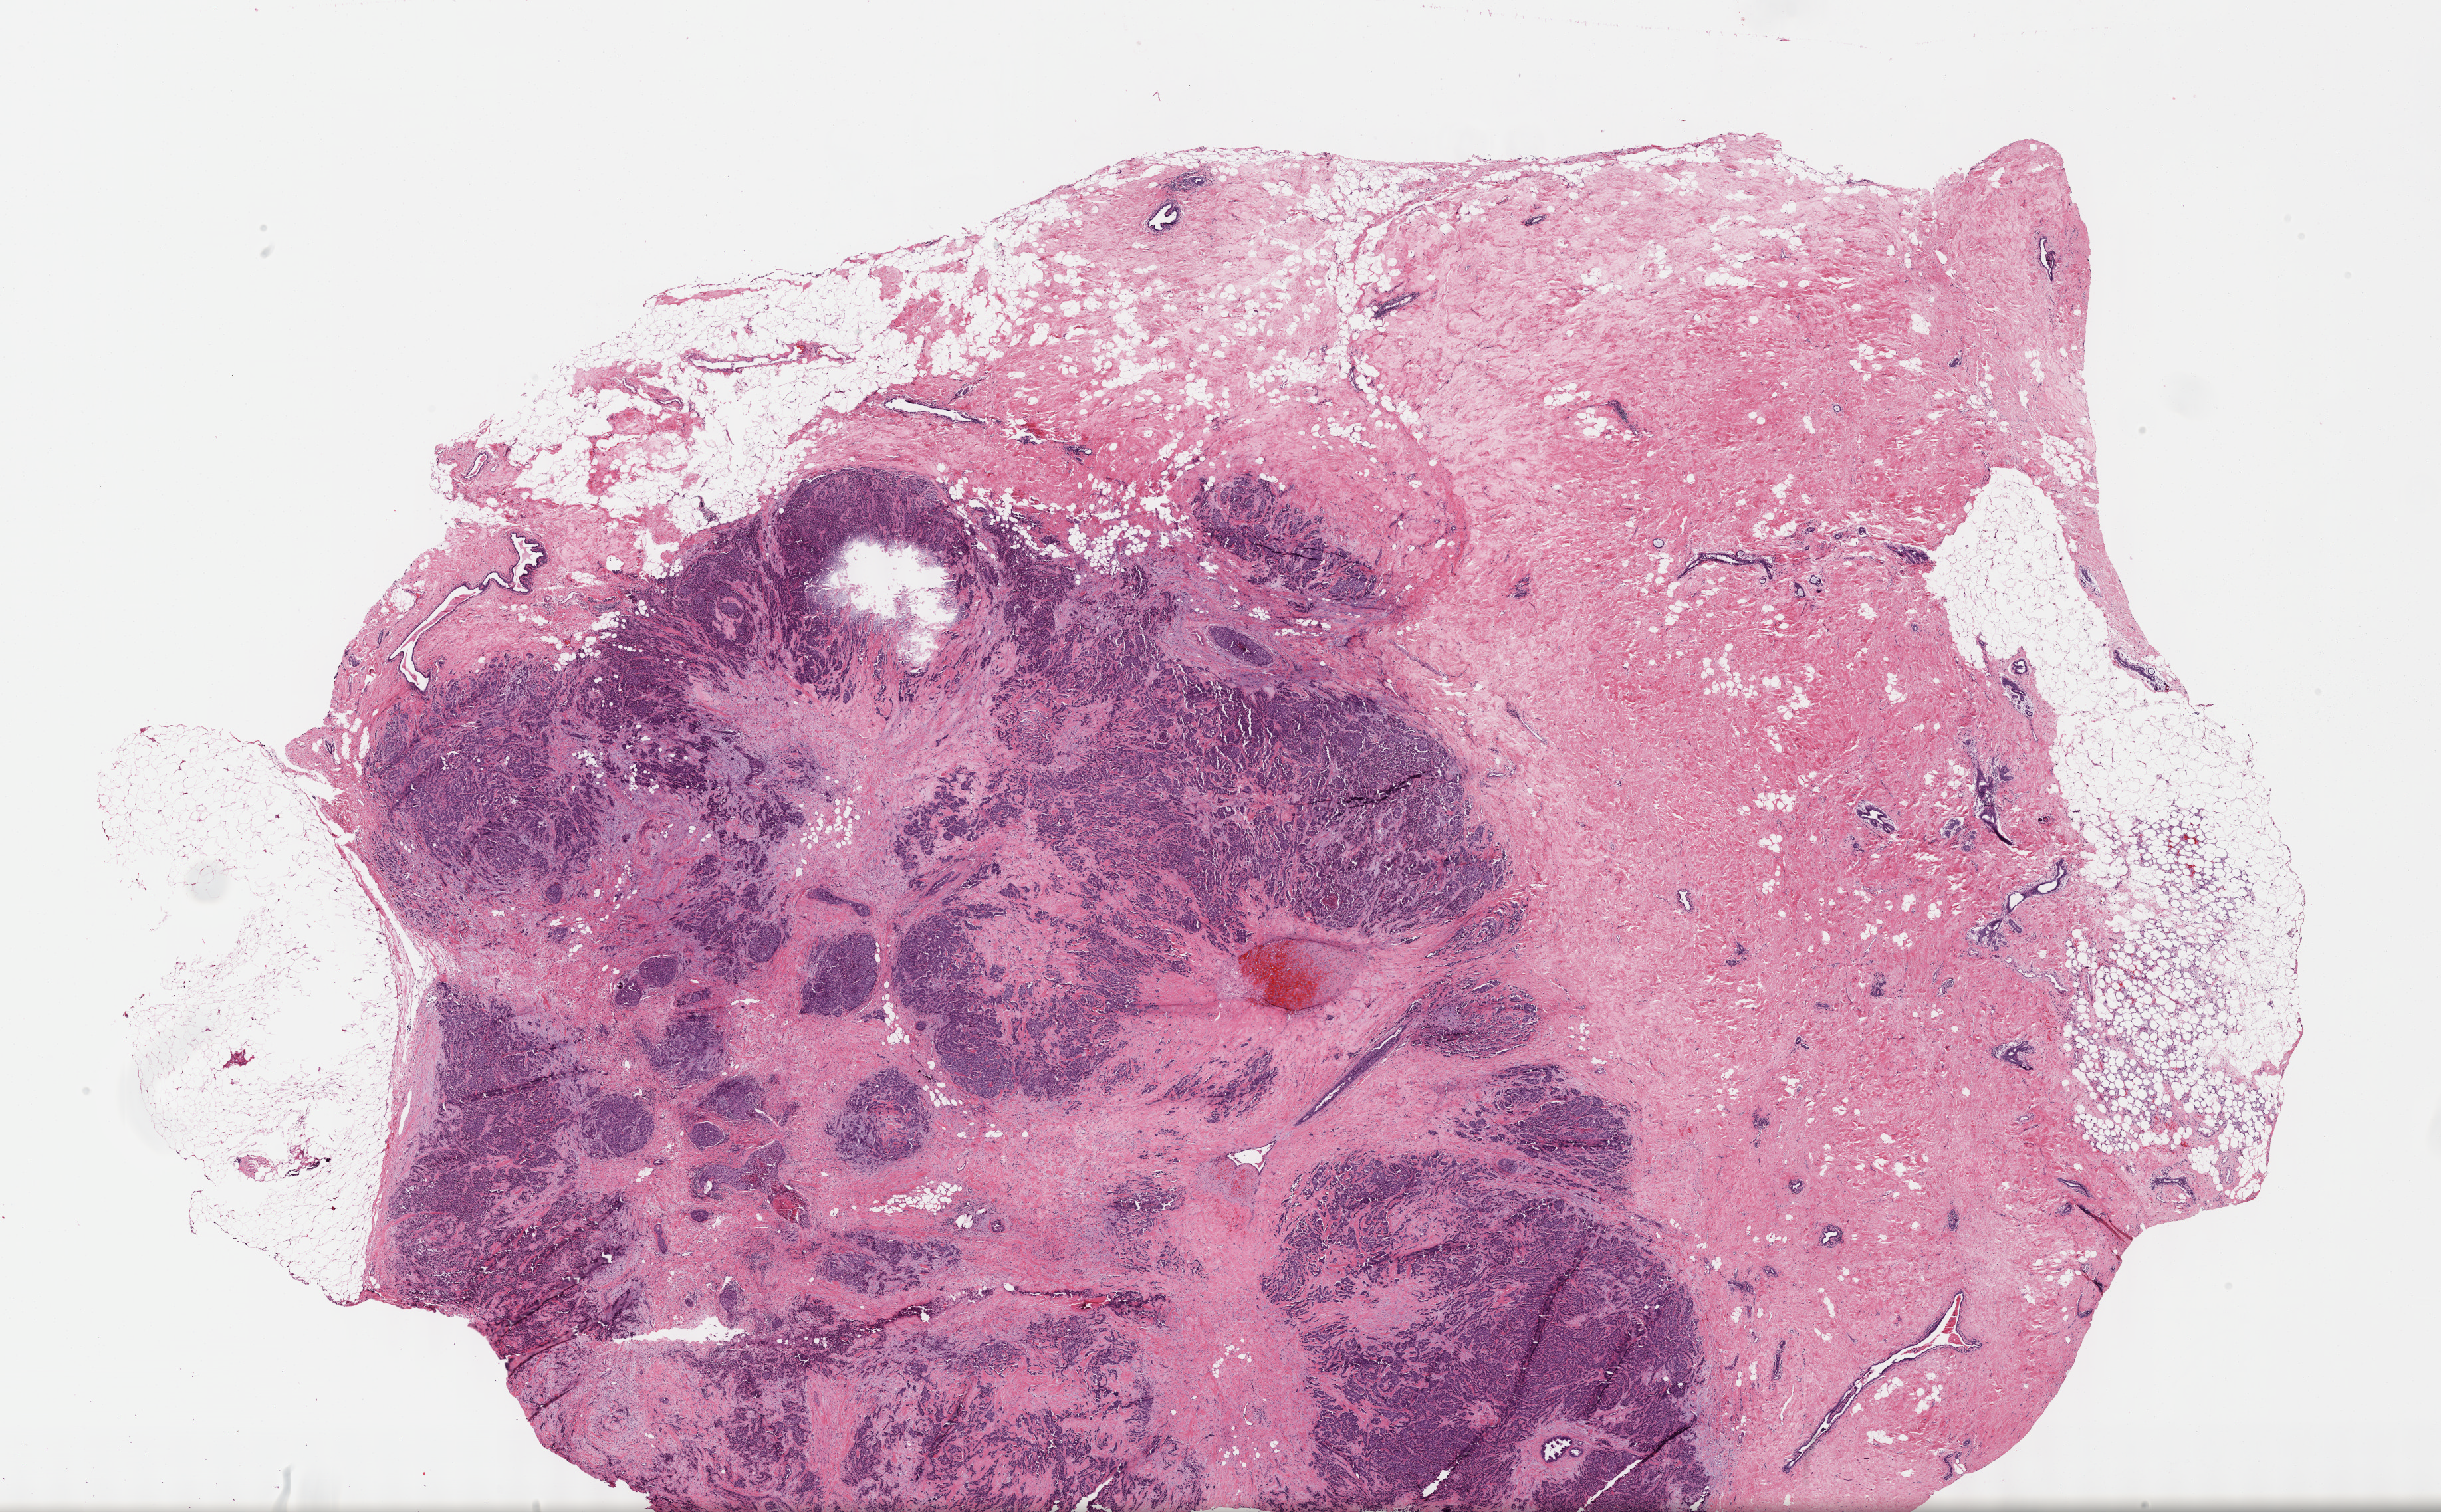
Digitized H&E tissue section (whole slide) — shown as a low-resolution overview of the whole scanned area (about 29.7 x 18.4 mm); FFPE section; sample: primary tumour, breast. Female patient; age at initial diagnosis 73 years.
Pathologic diagnosis: Infiltrating duct carcinoma, NOS. AJCC pathologic stage: IIA (7th edition).